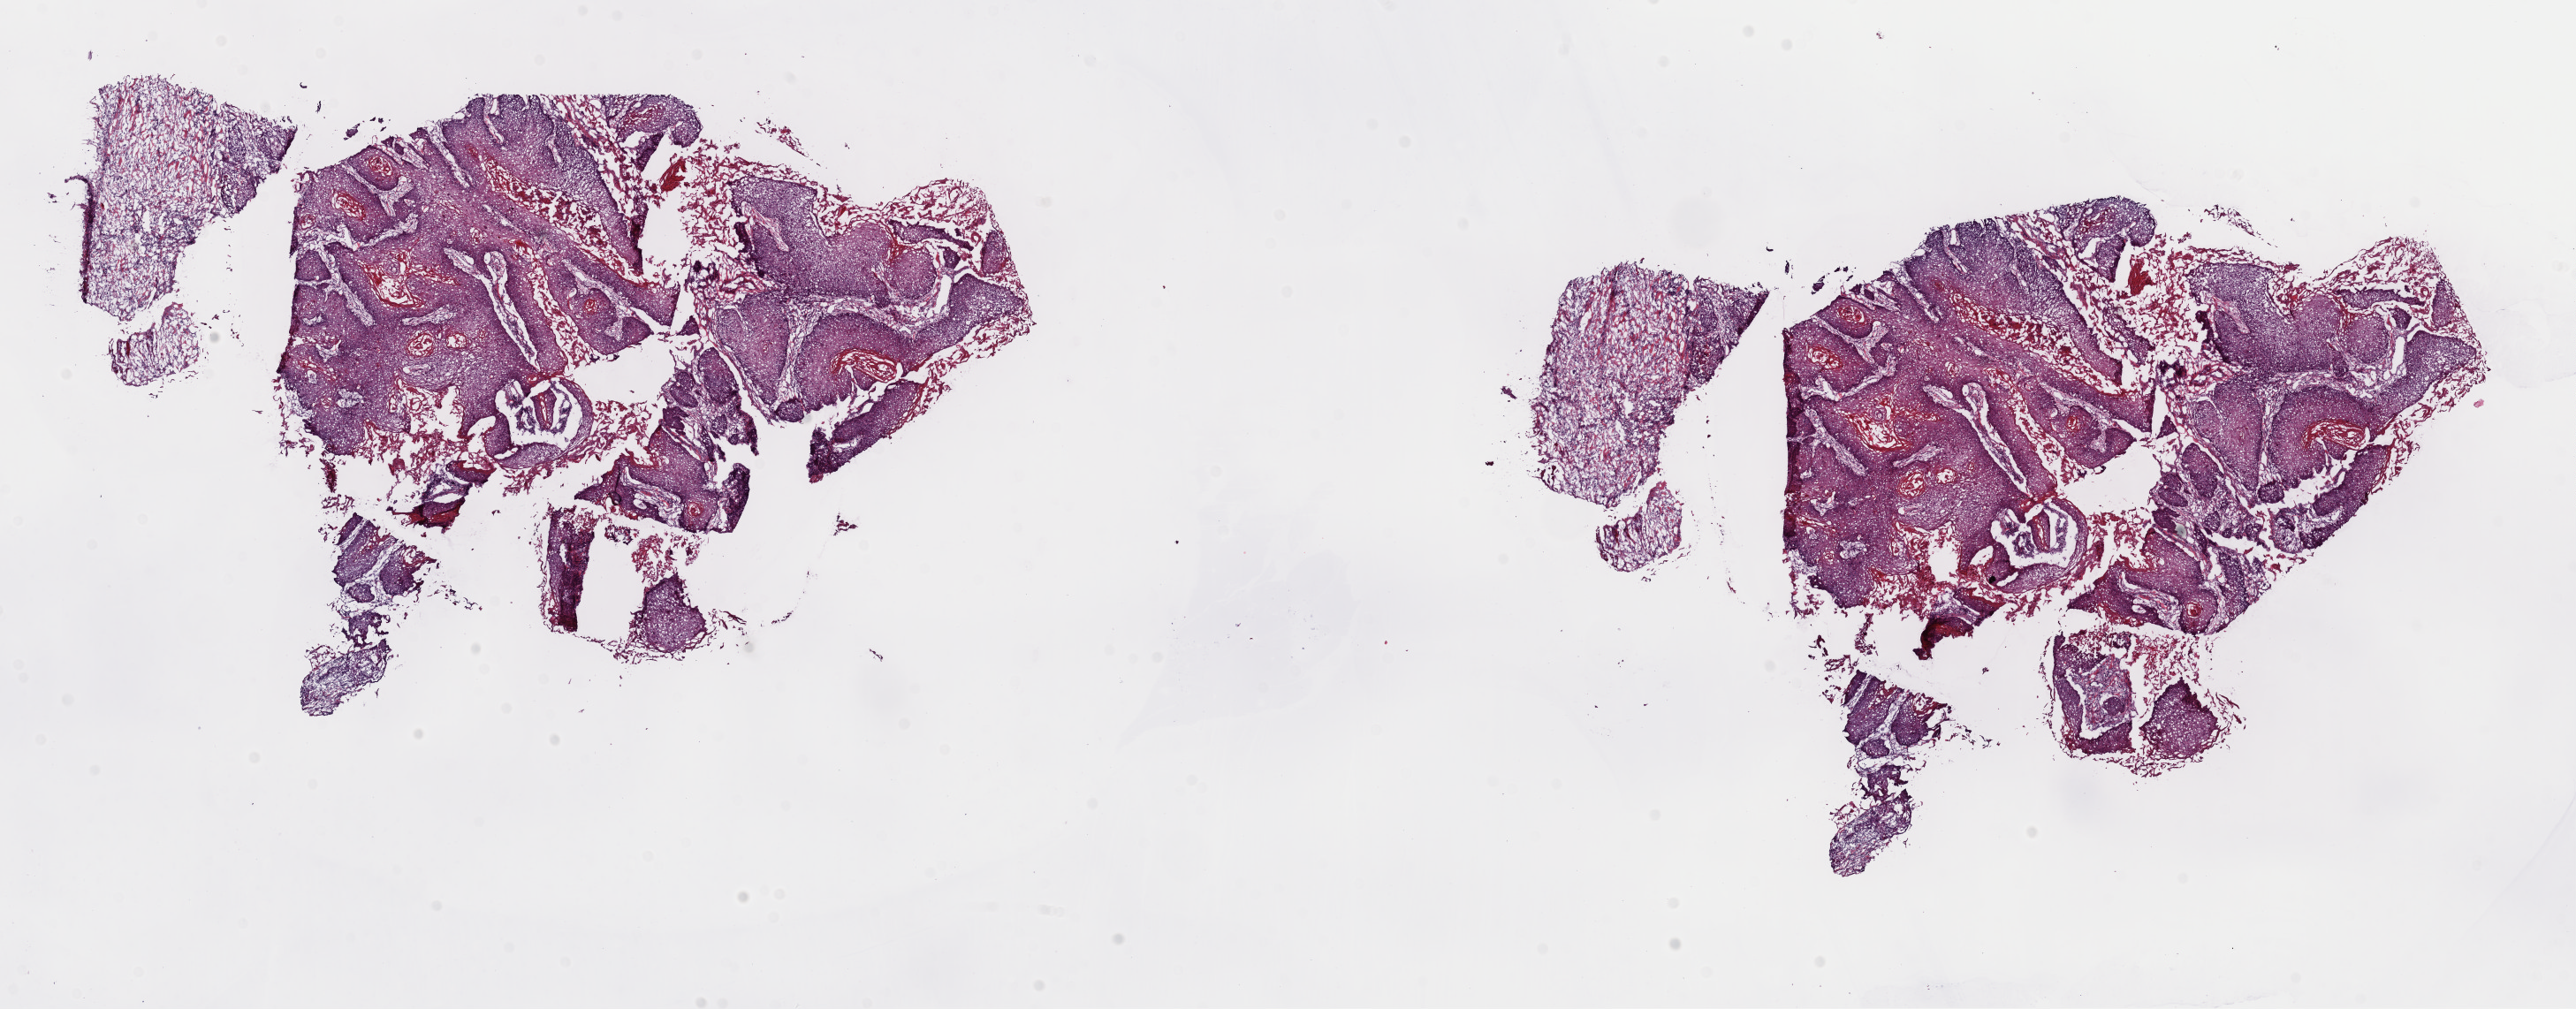
Hematoxylin and eosin (H&E) stained whole-slide image — shown as a low-resolution overview of the whole scanned area (about 23.0 x 9.0 mm); frozen section from the top of the tissue portion; head and neck, primary tumour sample. Patient: female, age at initial diagnosis 69 years. Histologic grade: G1 (well differentiated). Slide review estimates, as recorded: tumour cells 90%, tumour nuclei 90%, normal cells 5%, stromal cells 5%, necrosis 0%. Infiltration values recorded for this section: lymphocyte infiltration 5%, monocyte infiltration 0%, neutrophil infiltration 0%.
Pathologic diagnosis: Squamous cell carcinoma, NOS (mouth, NOS).